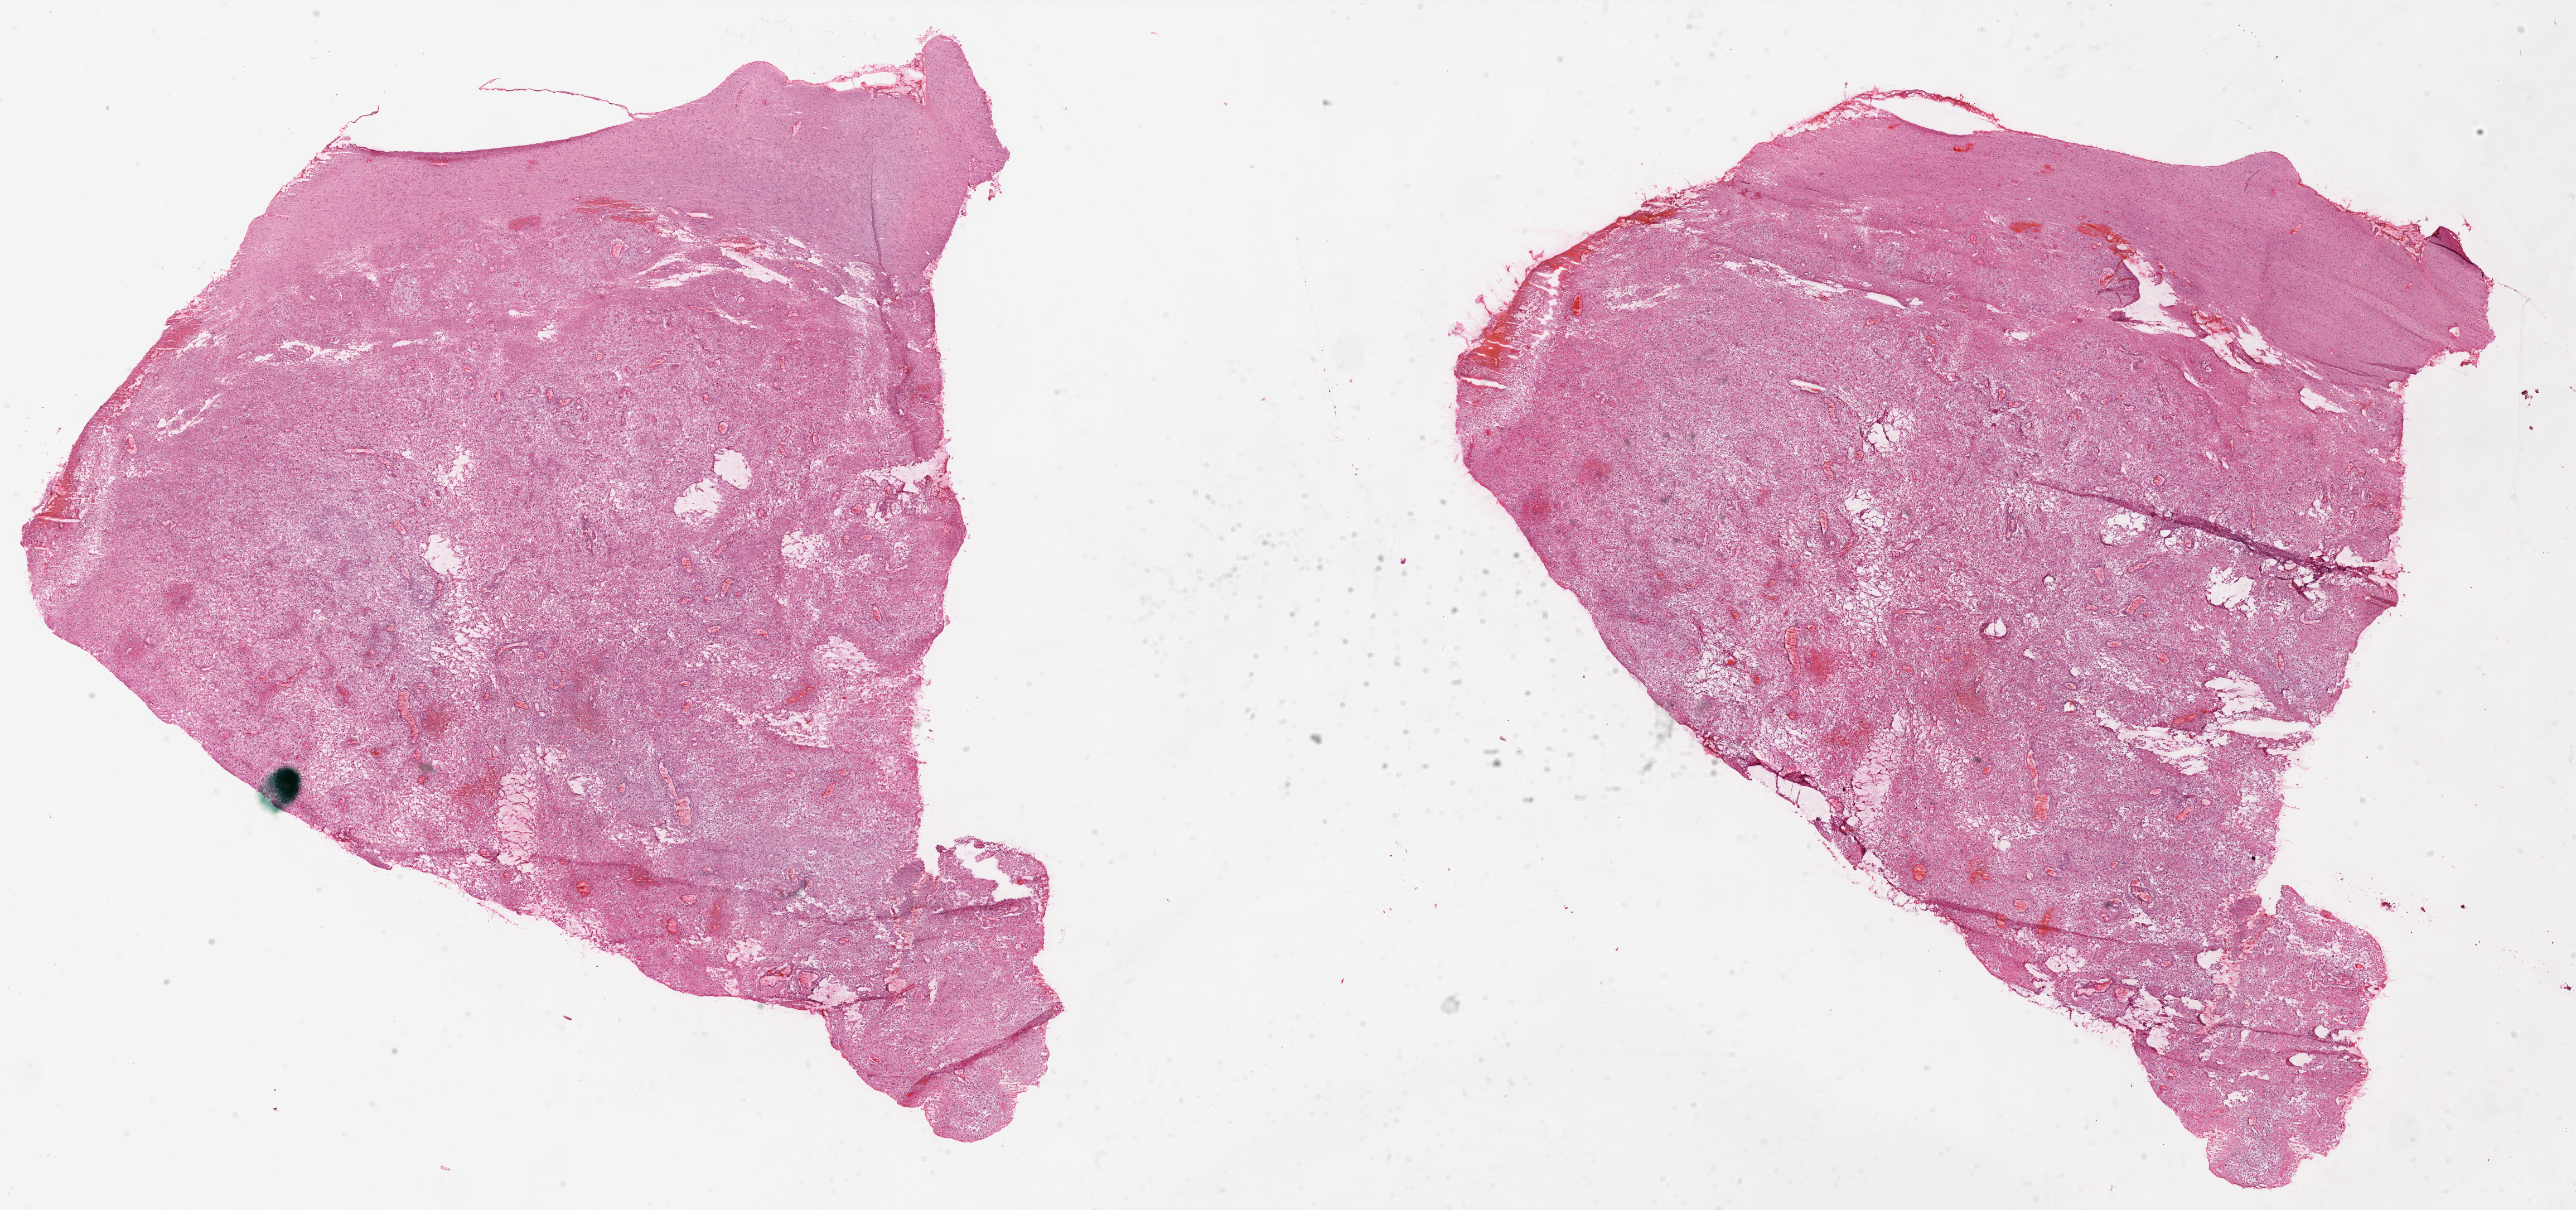
Digitized Hematoxylin and eosin (H&E) stained tissue section (whole slide) — whole scanned area (about 37.0 x 17.4 mm) shown as a low-resolution overview, frozen section from the top of the tissue portion, brain, primary tumour sample. Male, age 78 years at initial diagnosis. Pathologist review of this section (percent, as recorded): tumour cells 75%, tumour nuclei 90%, normal cells 0%, stromal cells 20%, necrosis 5%.
Pathologic diagnosis: Glioblastoma.